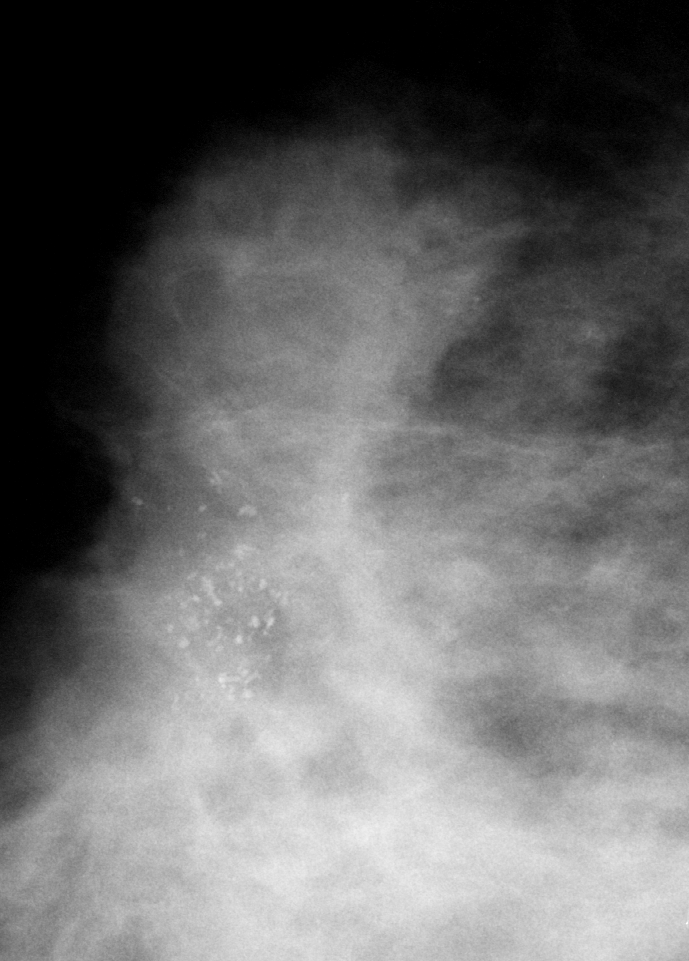
Region of interest cut from a scanned film mammogram (one marked finding); right breast; MLO view; BI-RADS breast density category 3 (scale 1–4).
- Marked abnormality: calcifications, morphology pleomorphic, distribution clustered; BI-RADS assessment category 5; subtlety rating 5 on a 1 (subtle) to 5 (obvious) scale; pathology (as recorded): malignant.